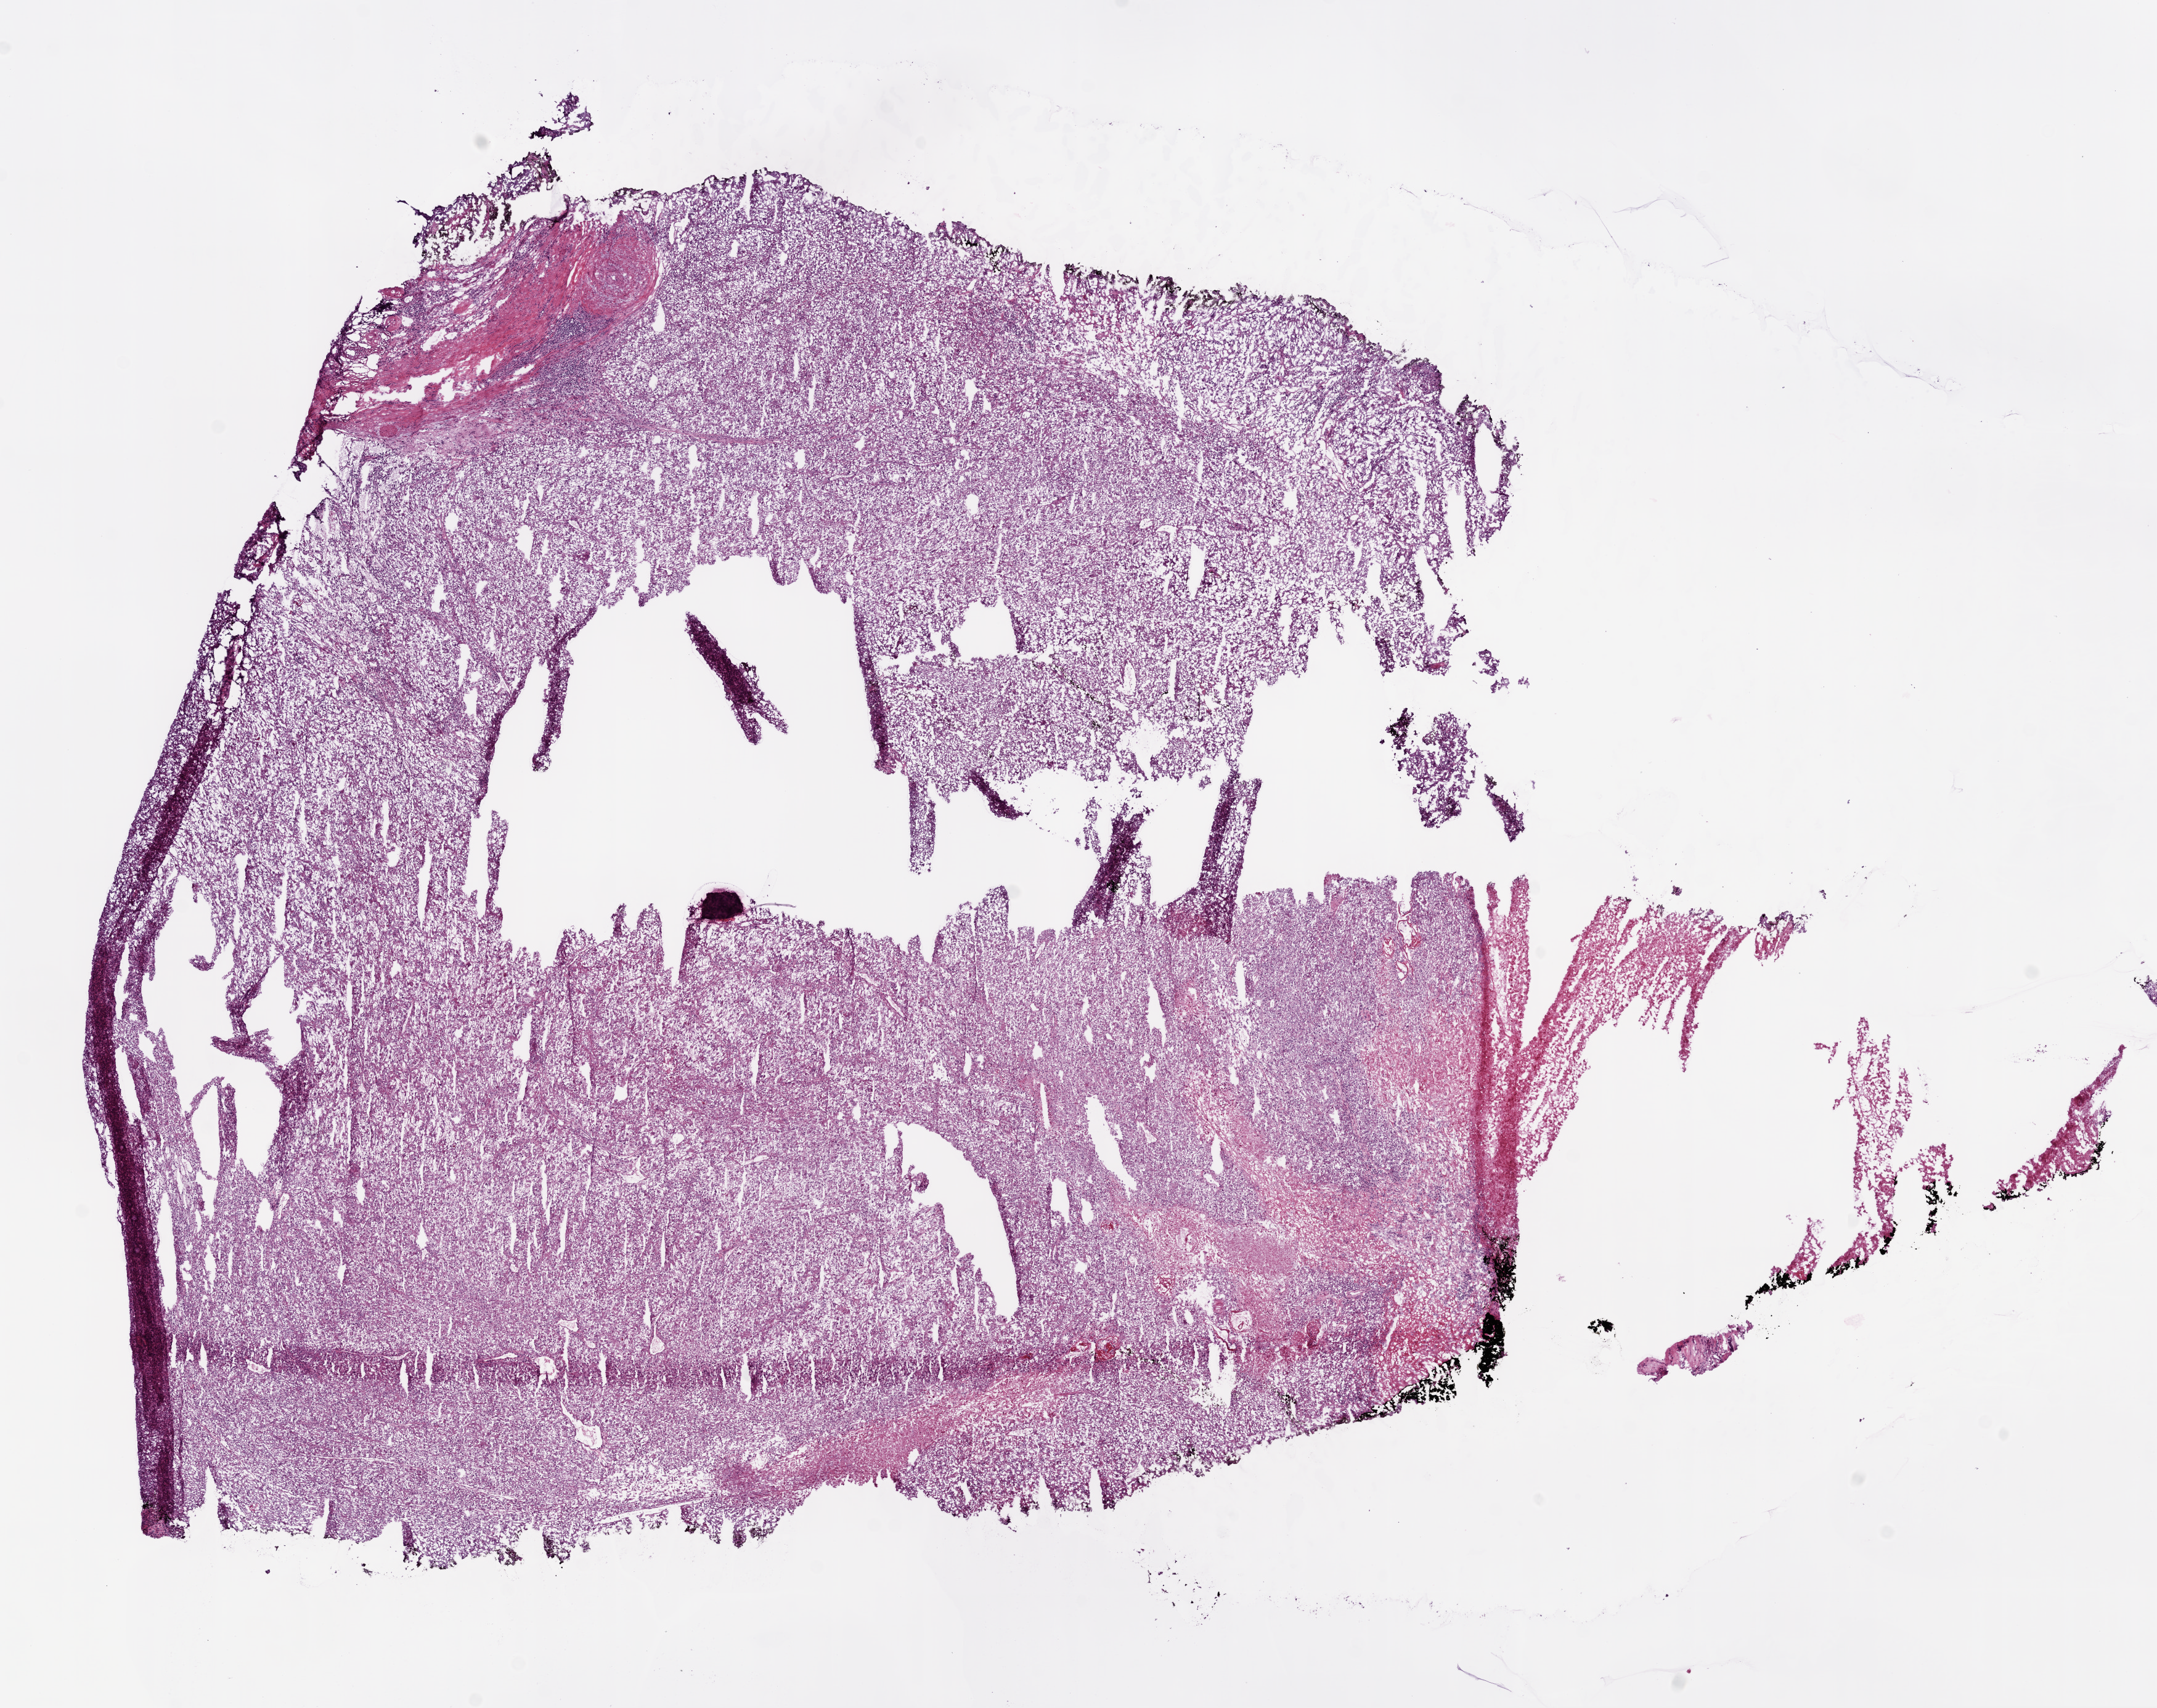
Digitized H&E tissue section (whole slide), a low-resolution overview of the entire scanned area, about 14.0 x 11.1 mm (acquisition: 20x scan); frozen section from the bottom of the tissue portion; sample: primary tumour, kidney. Male patient; age at initial diagnosis 70 years. Histologic grade: G2 (moderately differentiated). Pathologist review of this section (percent, as recorded): tumour cells 90%, tumour nuclei 80%, normal cells 0%, stromal cells 10%, necrosis 0%.
AJCC pathologic stage: I. TNM: T1b NX M0. Pathologic diagnosis: Clear cell adenocarcinoma, NOS.